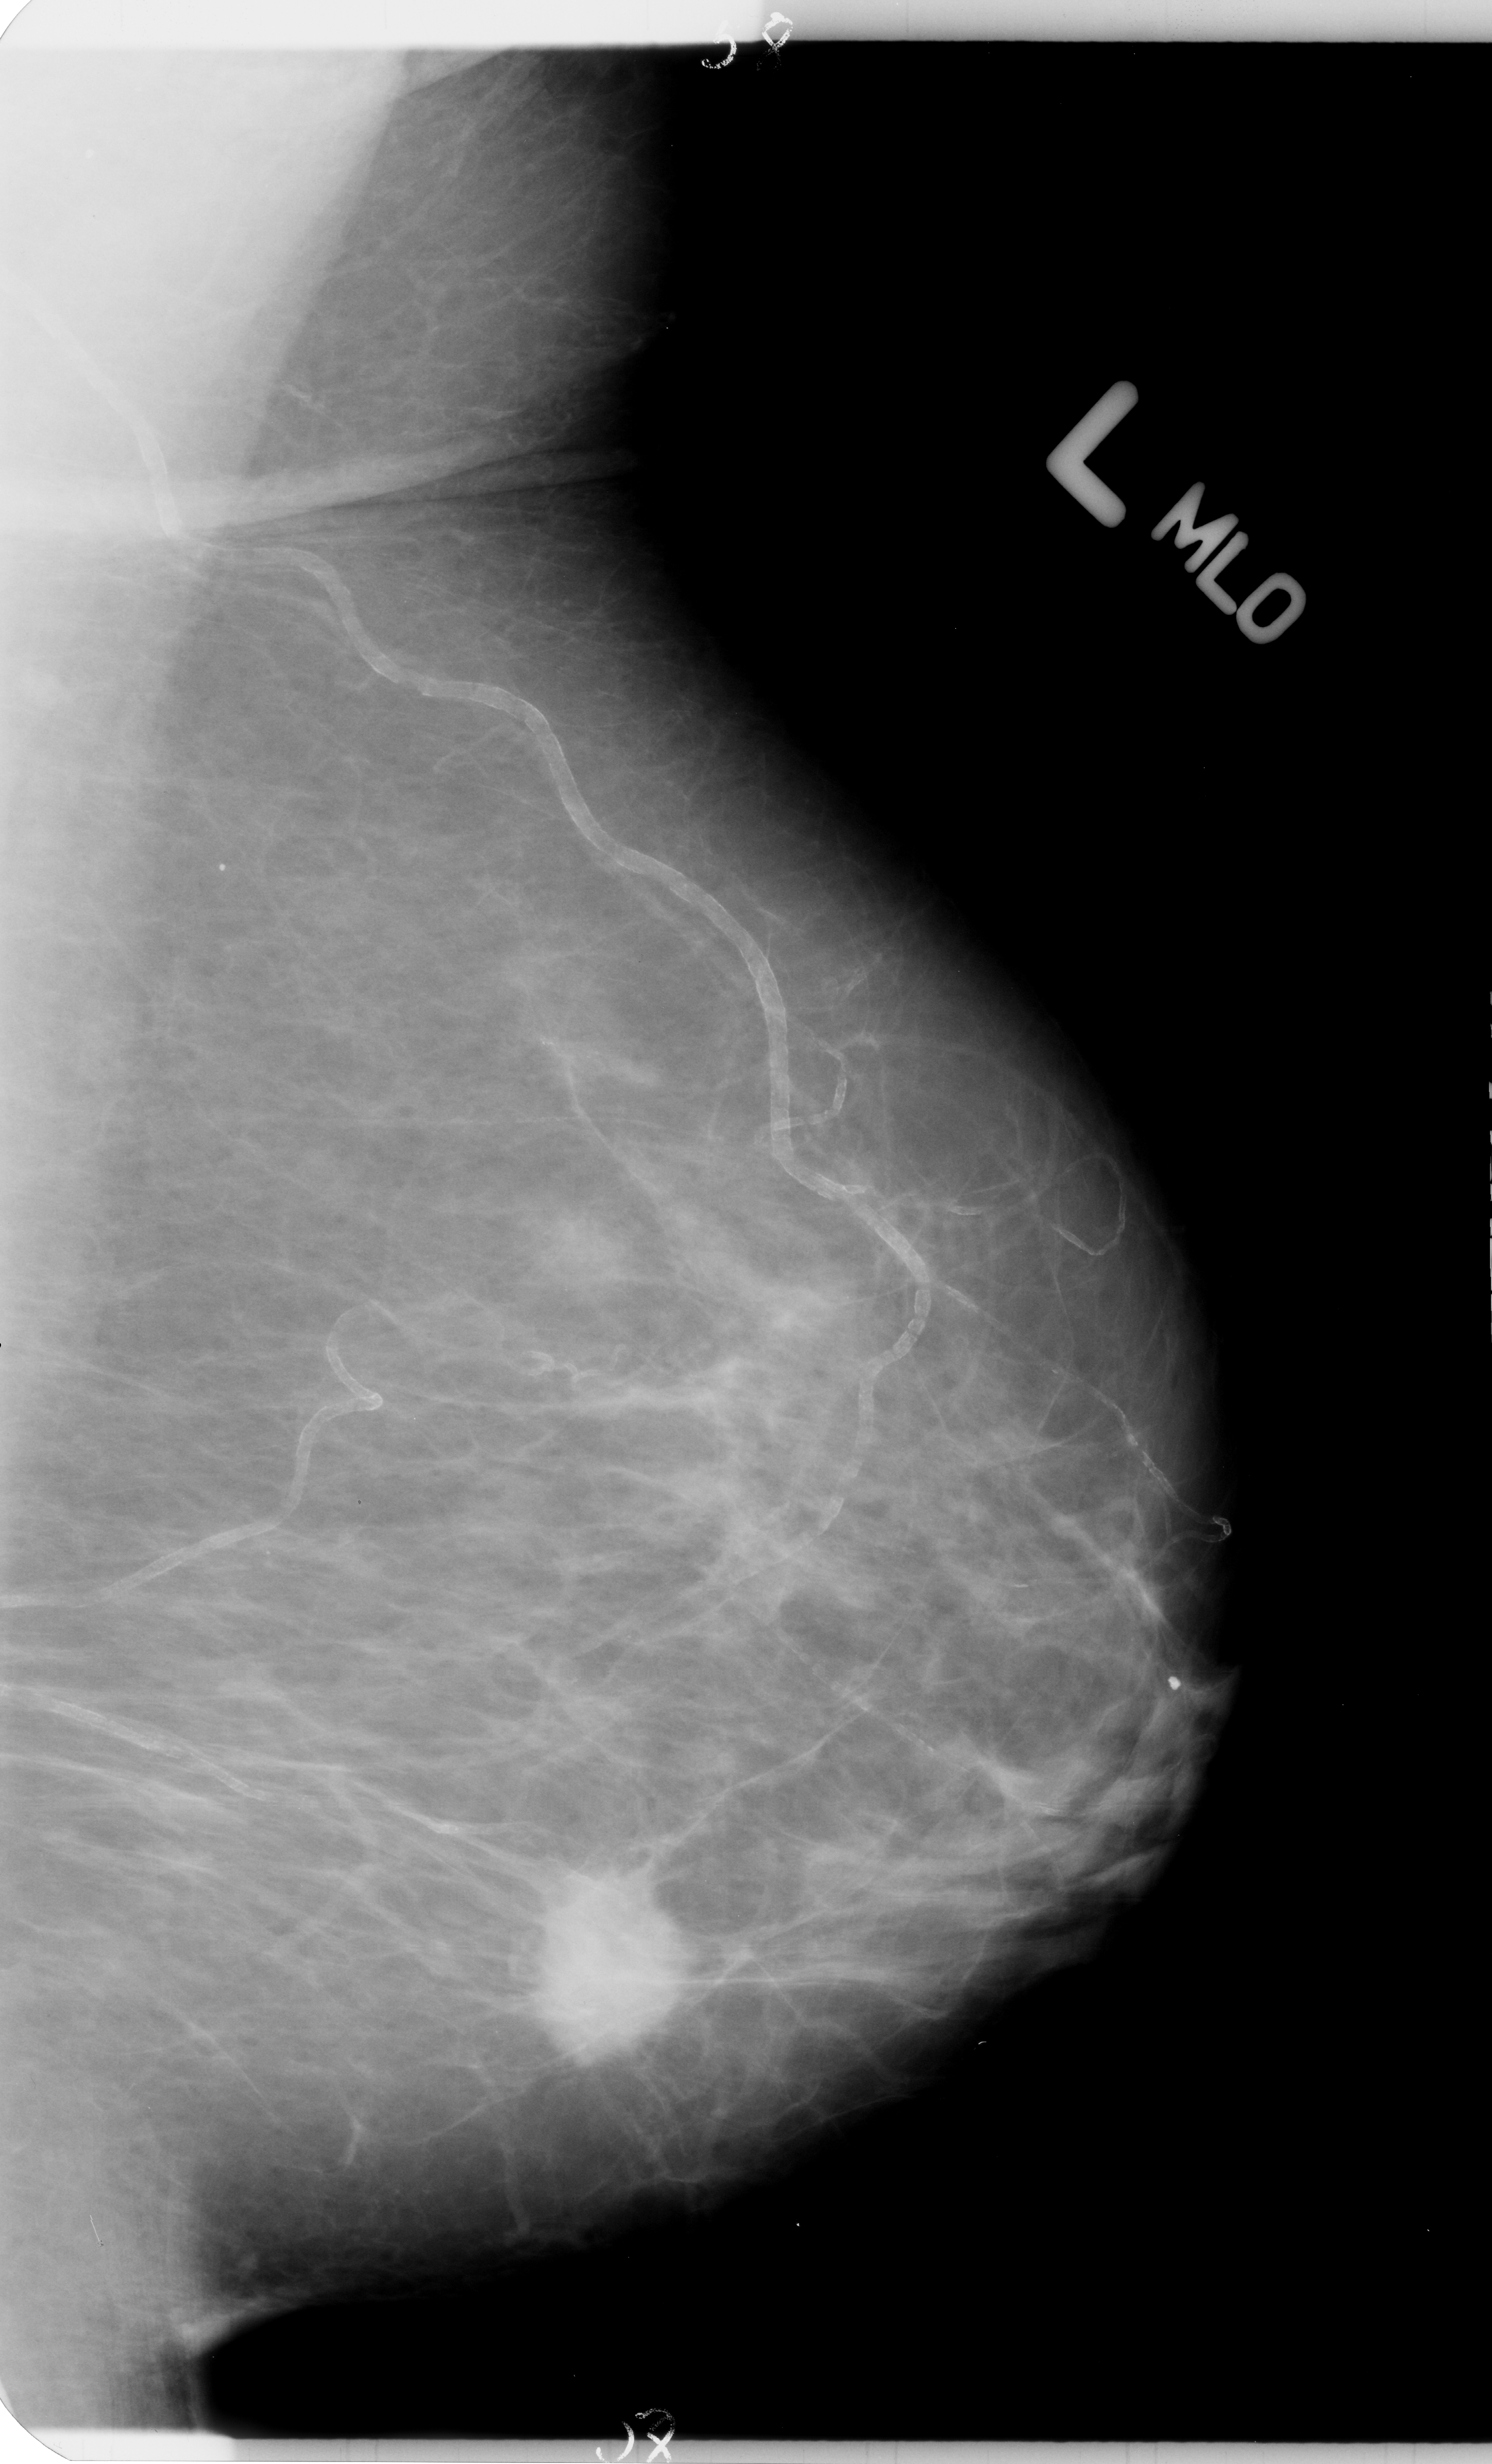
Scanned film-screen mammogram; left breast; mediolateral oblique (MLO) view; BI-RADS breast density category 2 (scale 1–4).
Radiologist-marked abnormalities on this image: mass, shape round, margins spiculated; BI-RADS assessment category 4; pathology (as recorded): malignant.